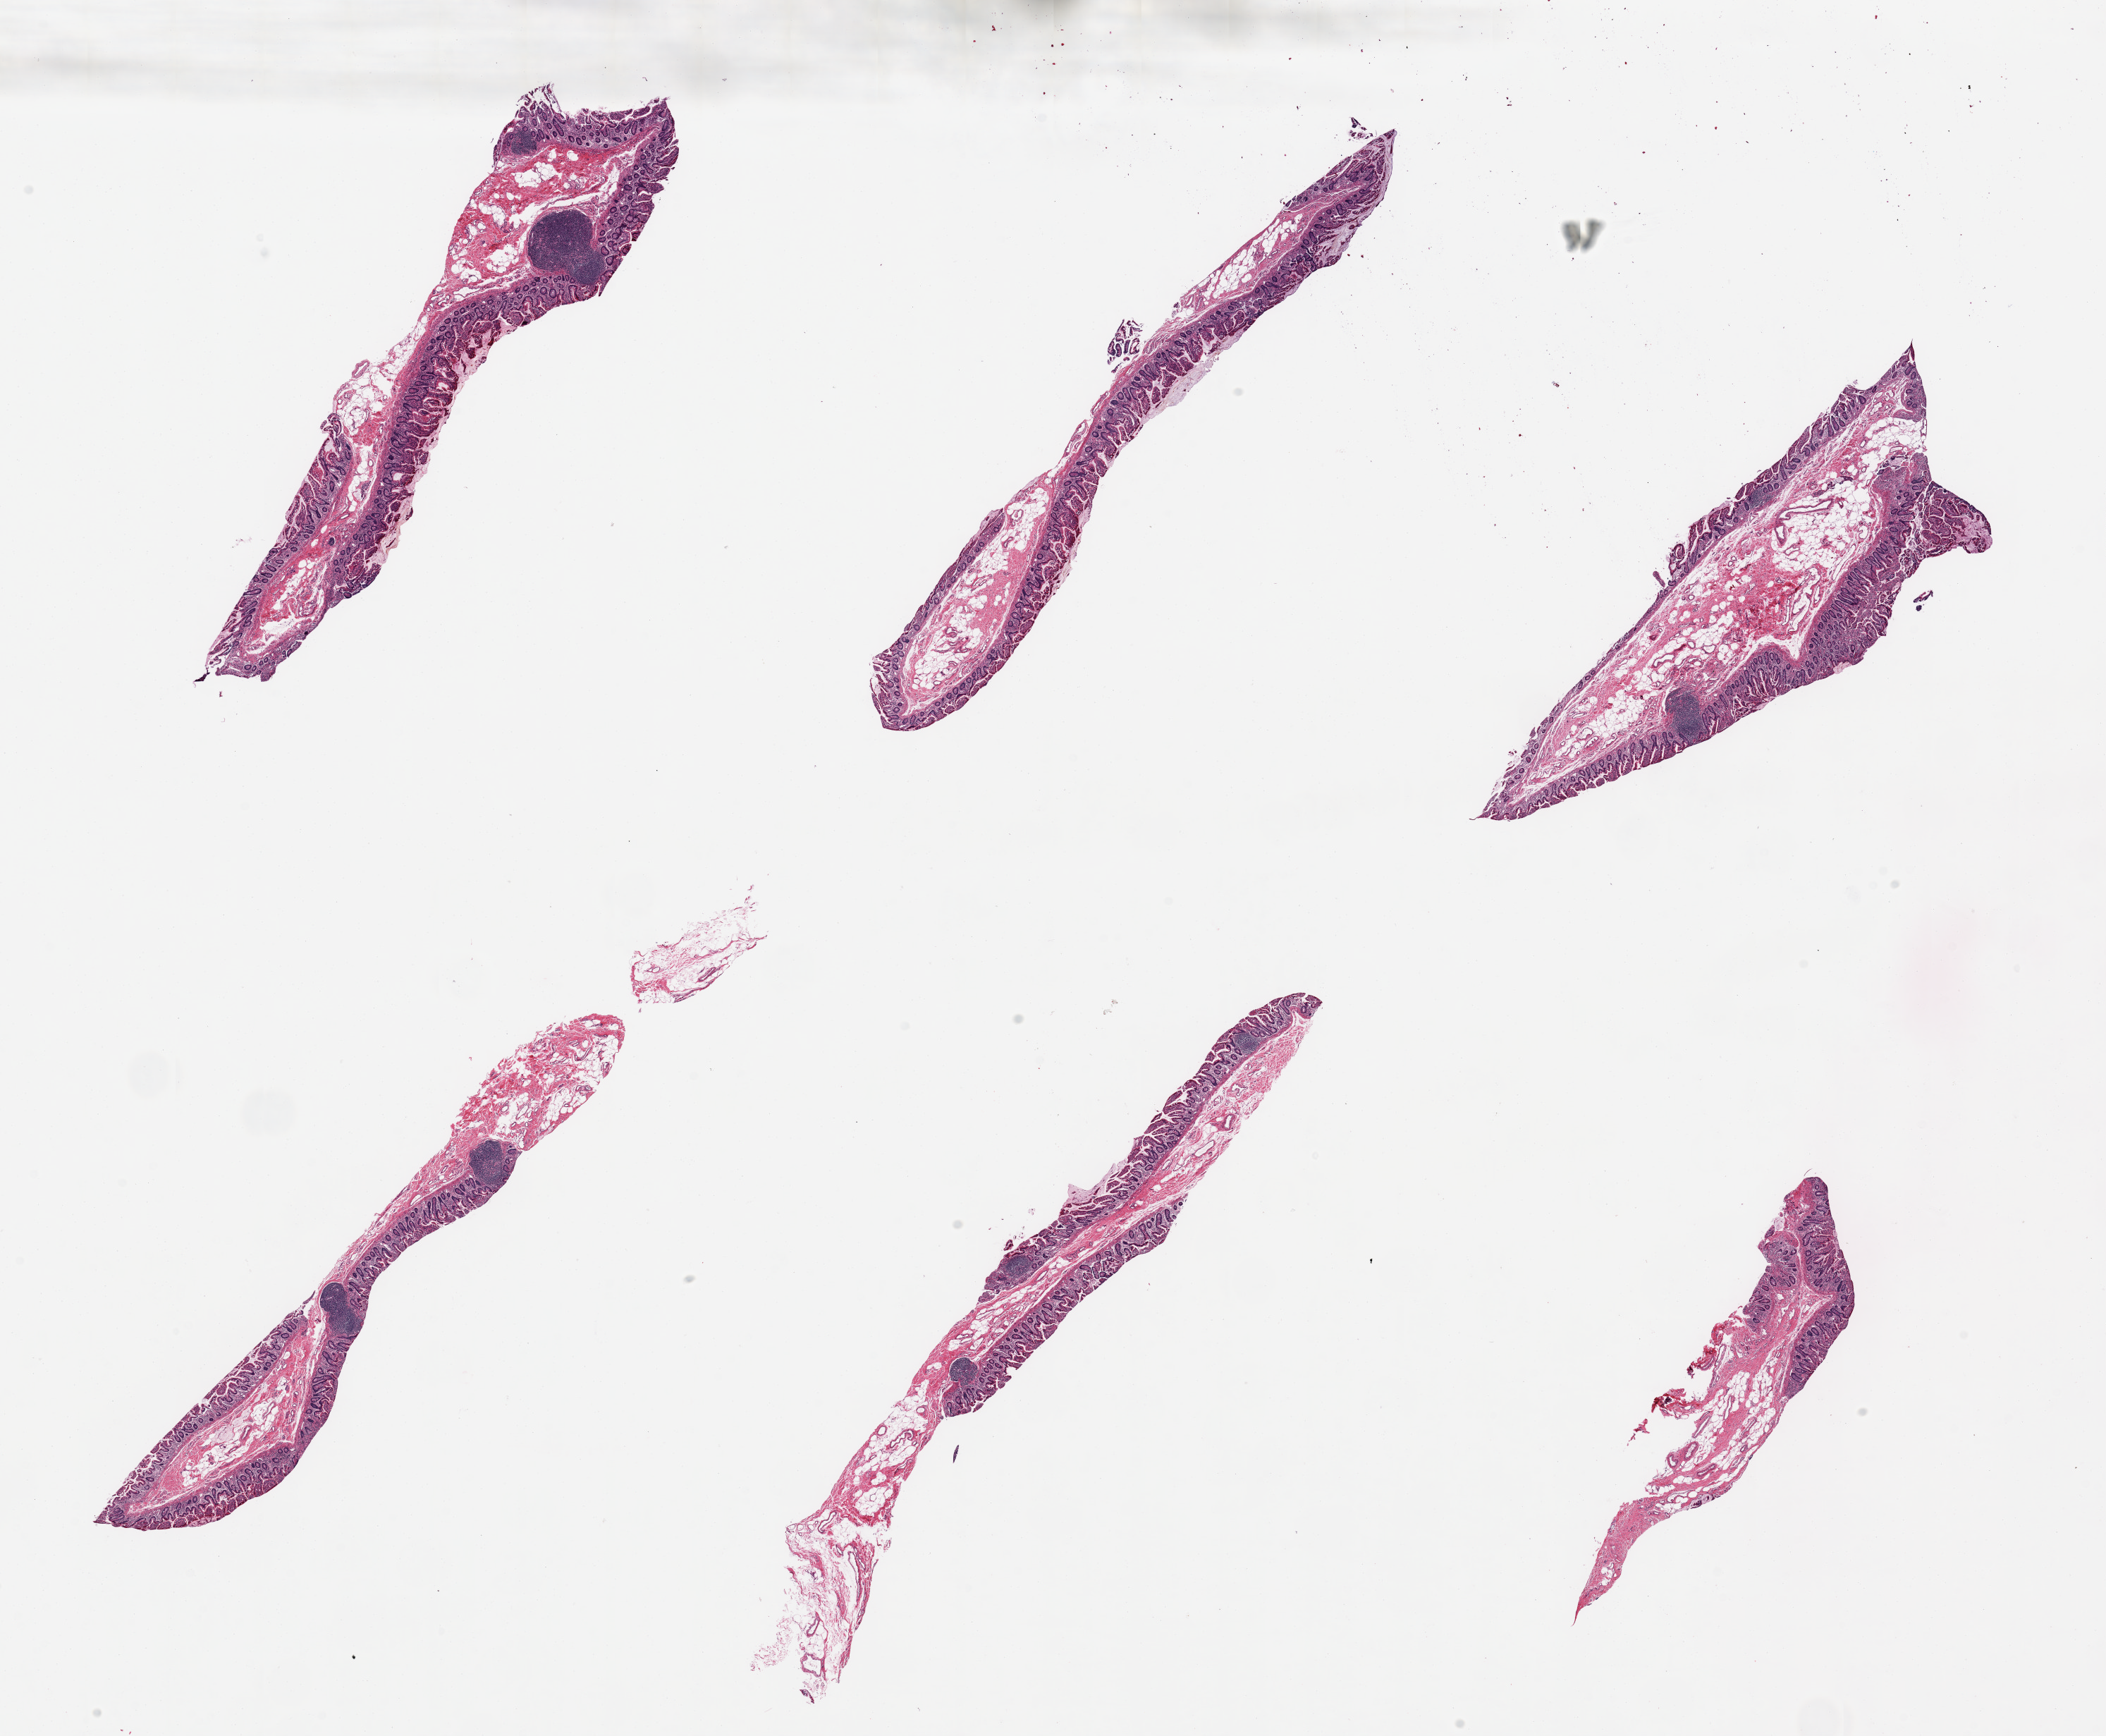
Whole-slide image, H&E stain, brightfield, a low-resolution overview of the entire scanned area, about 23.6 x 19.5 mm. PAXgene-fixed paraffin-embedded (PFPE) section. Section of ileum (target tissue). Donor tissue sample. Male donor.
- review note (as recorded): 6 pieces; mucosa/submucosa with scattered lymphoid aggregates